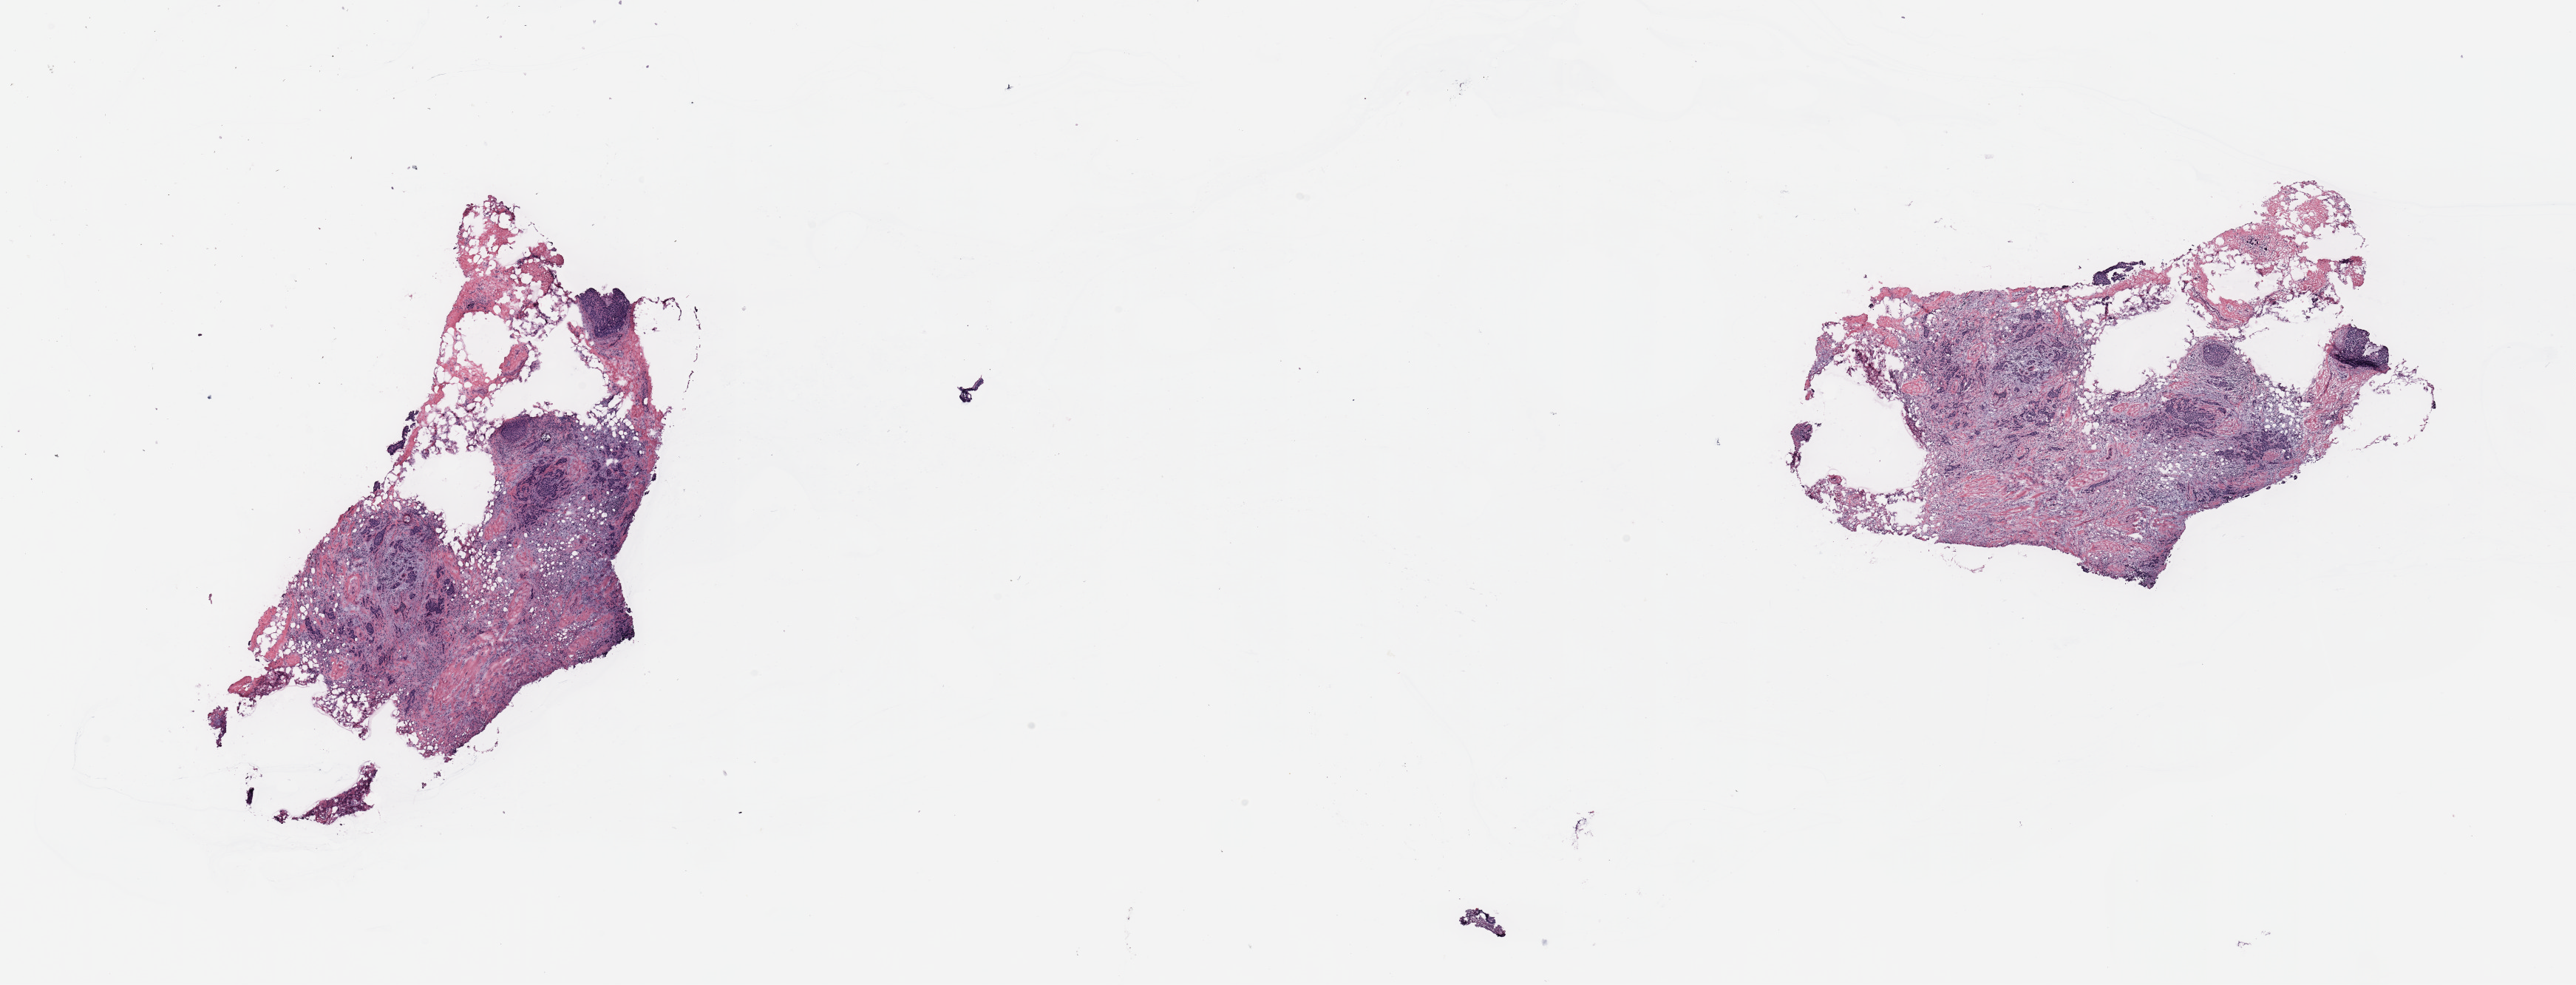
Digitized H&E tissue section (whole slide), a low-resolution overview of the entire scanned area, about 27.6 x 10.5 mm, breast, tissue type not recorded.
Patient diagnosis (cohort enrolment): breast cancer (breast).